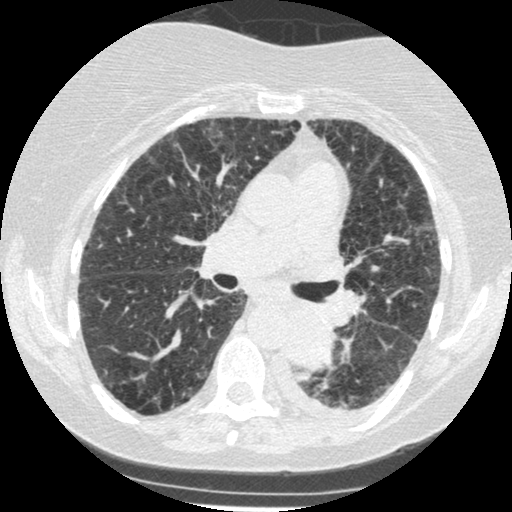
Low-dose screening chest CT, one axial slice; position 146 of 341 along the scan axis; reconstruction kernel STANDARD; 120 kVp; lung window (W 1500 / L -600 HU); 1.25 mm slice thickness; 512 × 512 image matrix.
Outlined on this slice (manually delineated by an expert):
- lesion 1 (tumor, lower lobe of left lung): box from (x=286, y=308) to (x=335, y=368) px